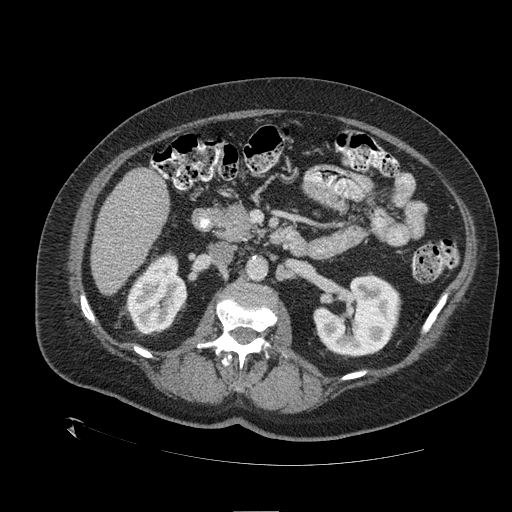
Contrast-enhanced abdominal CT (liver protocol), one axial slice. Slice 48 of 109 in the series (ordered by position). Reconstruction kernel STANDARD. 120 kVp. One of 2 acquisitions stored at this slice position. Soft-tissue window (W 400 / L 40 HU). 2.5 mm slice thickness. 512 × 512 image matrix, field of view 460 × 460 mm. From the clinical record (not read from this slice): diagnosis: hepatocellular carcinoma (patient treated with transarterial chemoembolisation; whether this scan precedes or follows treatment is not stated here); TNM stage (as recorded): Stage-I; Child-Pugh class: A; tumour differentiation: no biopsy; tumour size: 4.6 cm.
Annotated regions visible in this slice (semi-automatic segmentation, software-assisted and operator-edited):
- liver parenchyma outside the tumour (the mass and vessels are separate outlines, so this box may not span the whole liver): bounding box (x1, y1, x2, y2) in pixels: (90, 168, 170, 294)